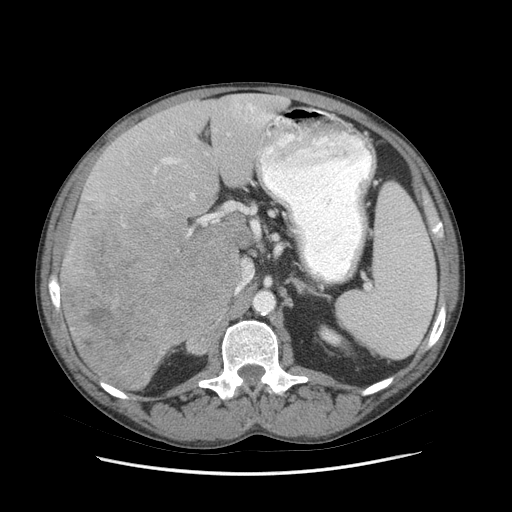
Contrast-enhanced abdominal CT (liver protocol), one axial slice. Slice 43 of 89 in the series (ordered by position). Reconstruction kernel STANDARD. 140 kVp. Soft-tissue window (W 400 / L 40 HU). 512 × 512 image matrix. From the clinical record (not read from this slice): diagnosis: hepatocellular carcinoma (patient treated with transarterial chemoembolisation; whether this scan precedes or follows treatment is not stated here); TNM stage (as recorded): Stage-IIIB; Child-Pugh class: A; tumour differentiation: moderately differentiated.
Annotated regions visible in this slice (semi-automatic segmentation, software-assisted and operator-edited):
- liver parenchyma outside the tumour (the mass and vessels are separate outlines, so this box may not span the whole liver): bounding box <60,94,287,390> (left, top, right, bottom; pixels)
- mass: <59,208,239,388>
- liver vessels: <88,103,274,223>